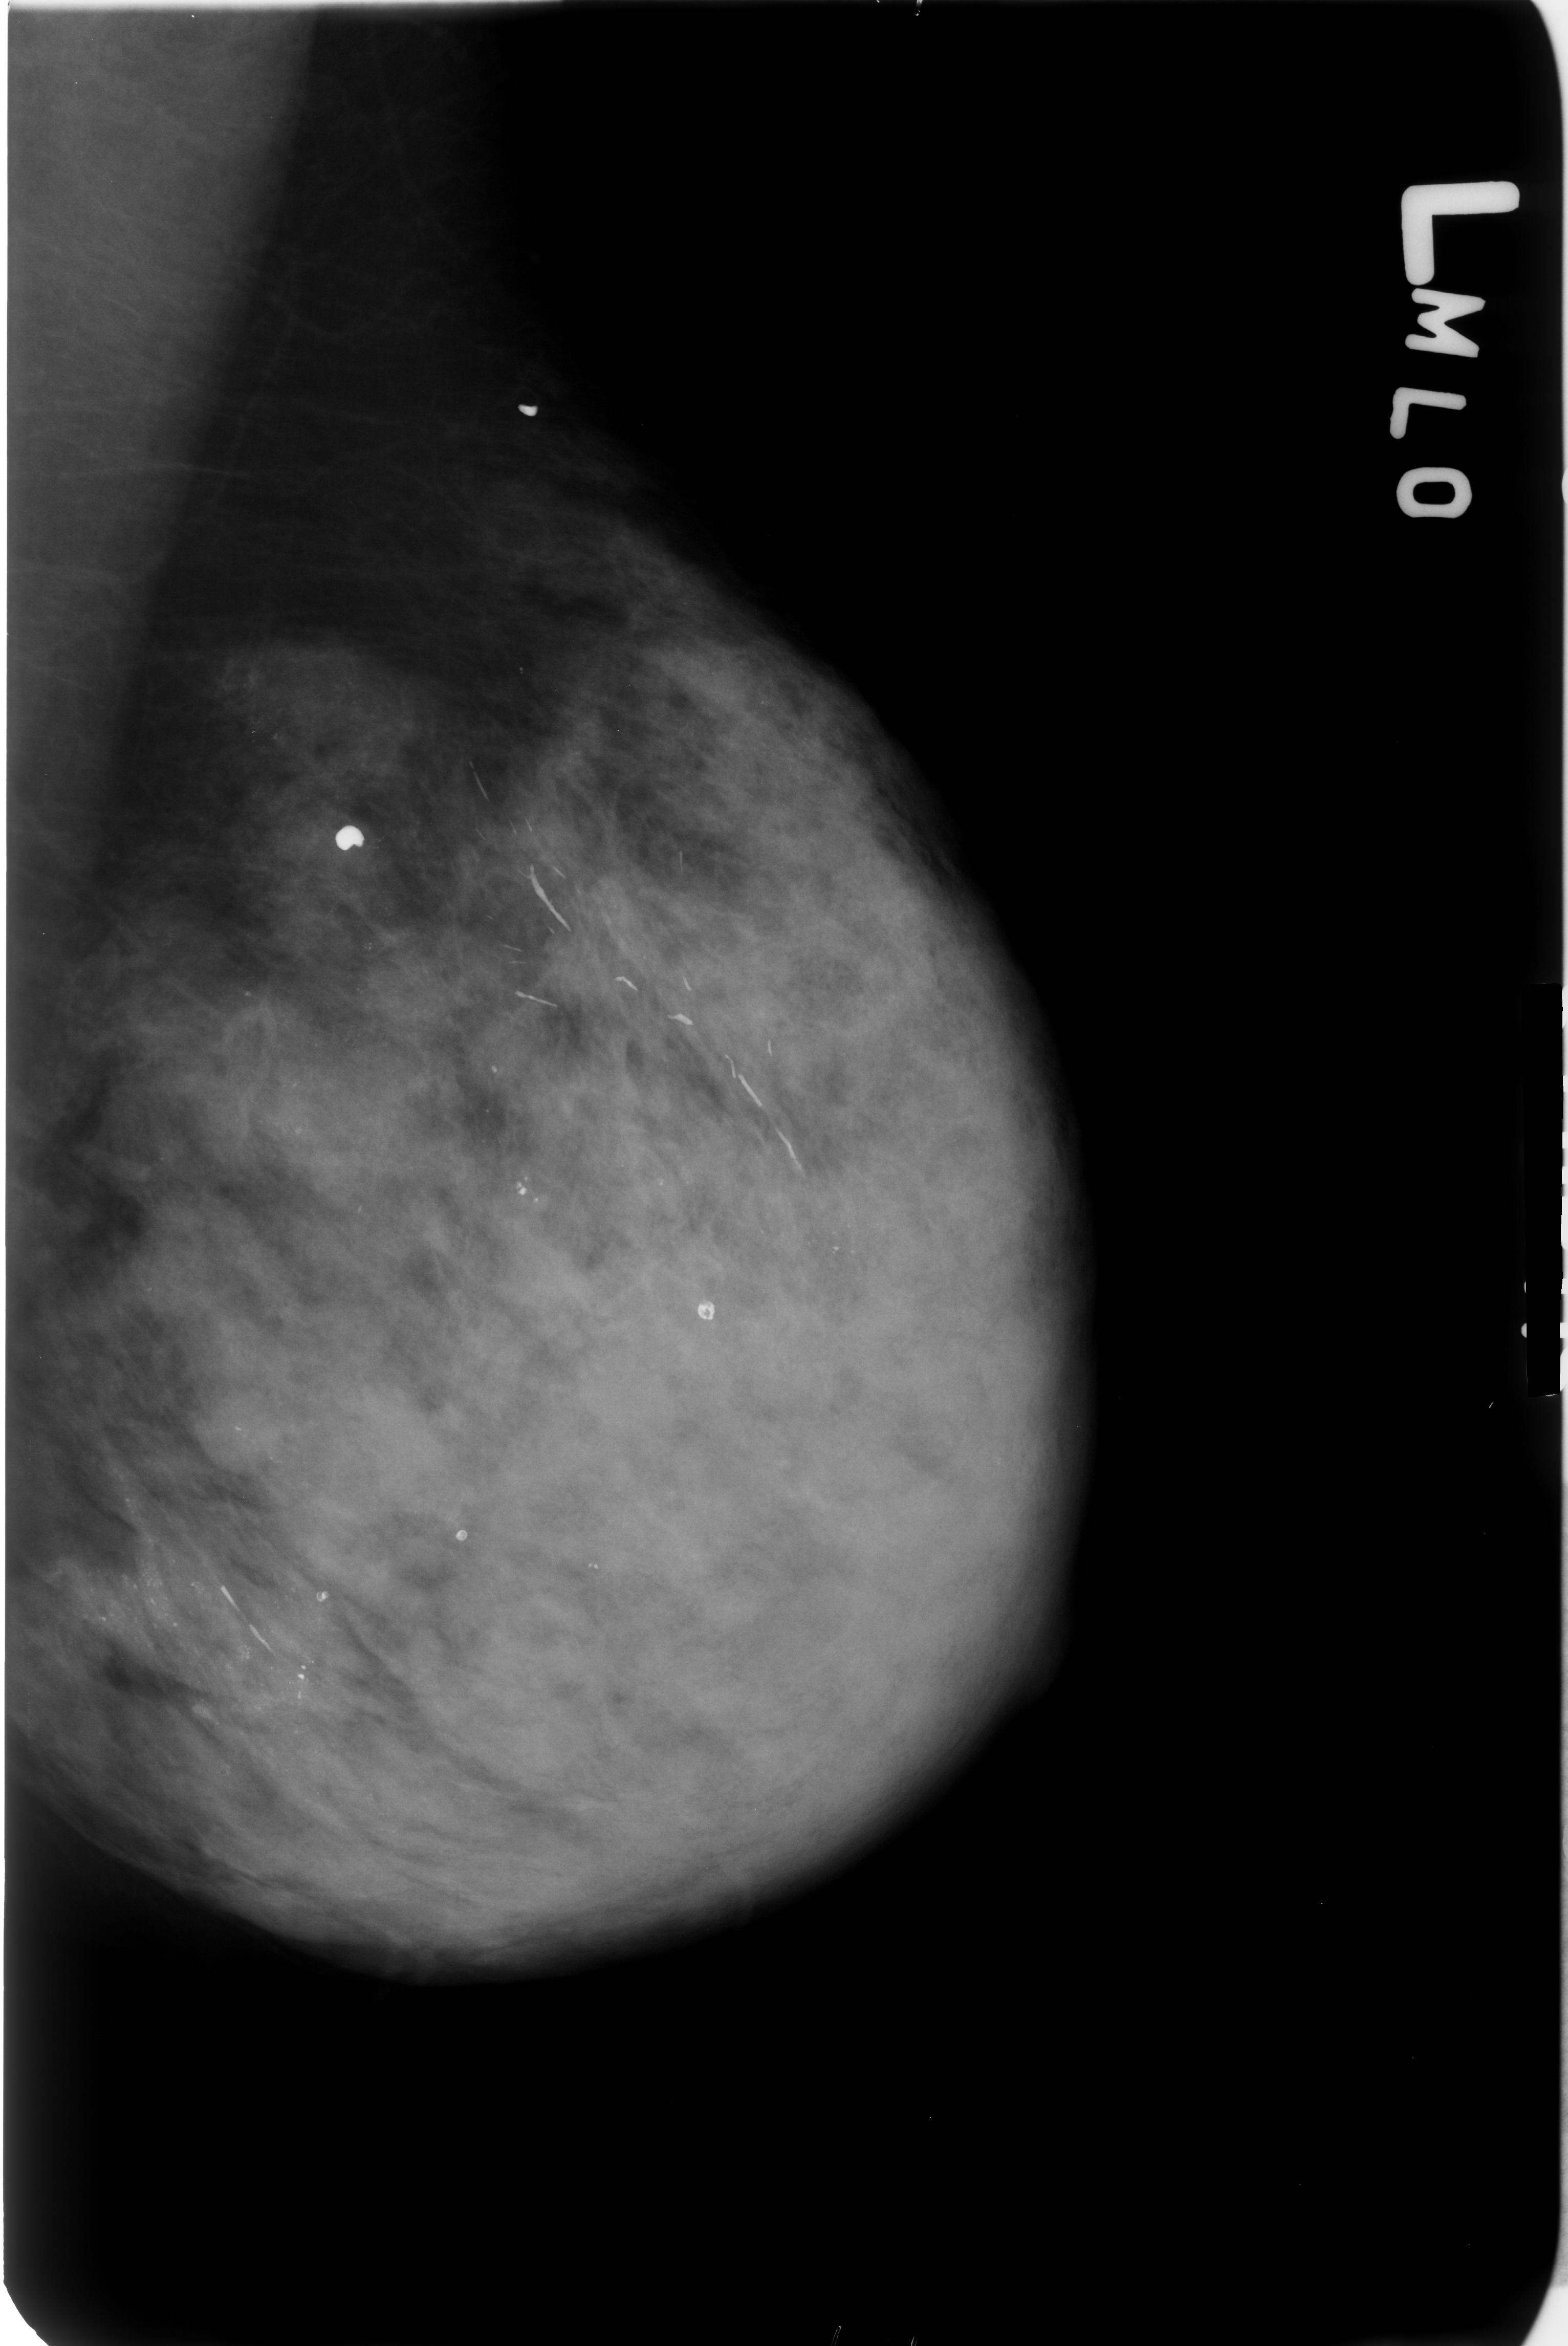
Digitized screen-film mammogram. Left breast. MLO view. 1568 × 2346 image matrix.
Marked abnormalities (boxes around the expert regions of interest):
- Finding 1 of 2: calcifications, morphology punctate / lucent center, distribution regional; BI-RADS assessment category 2; outcome (as recorded, no biopsy): benign without callback (not worked up further): bounding box <171,1559,349,1749> (left, top, right, bottom; pixels)
- Finding 2 of 2: calcifications, morphology punctate / lucent center, distribution regional; BI-RADS assessment category 2; subtlety rating 5 on a 1 (subtle) to 5 (obvious) scale; benign; no additional work-up was recommended (outcome (as recorded, no biopsy): benign without callback): <503,843,840,1205>